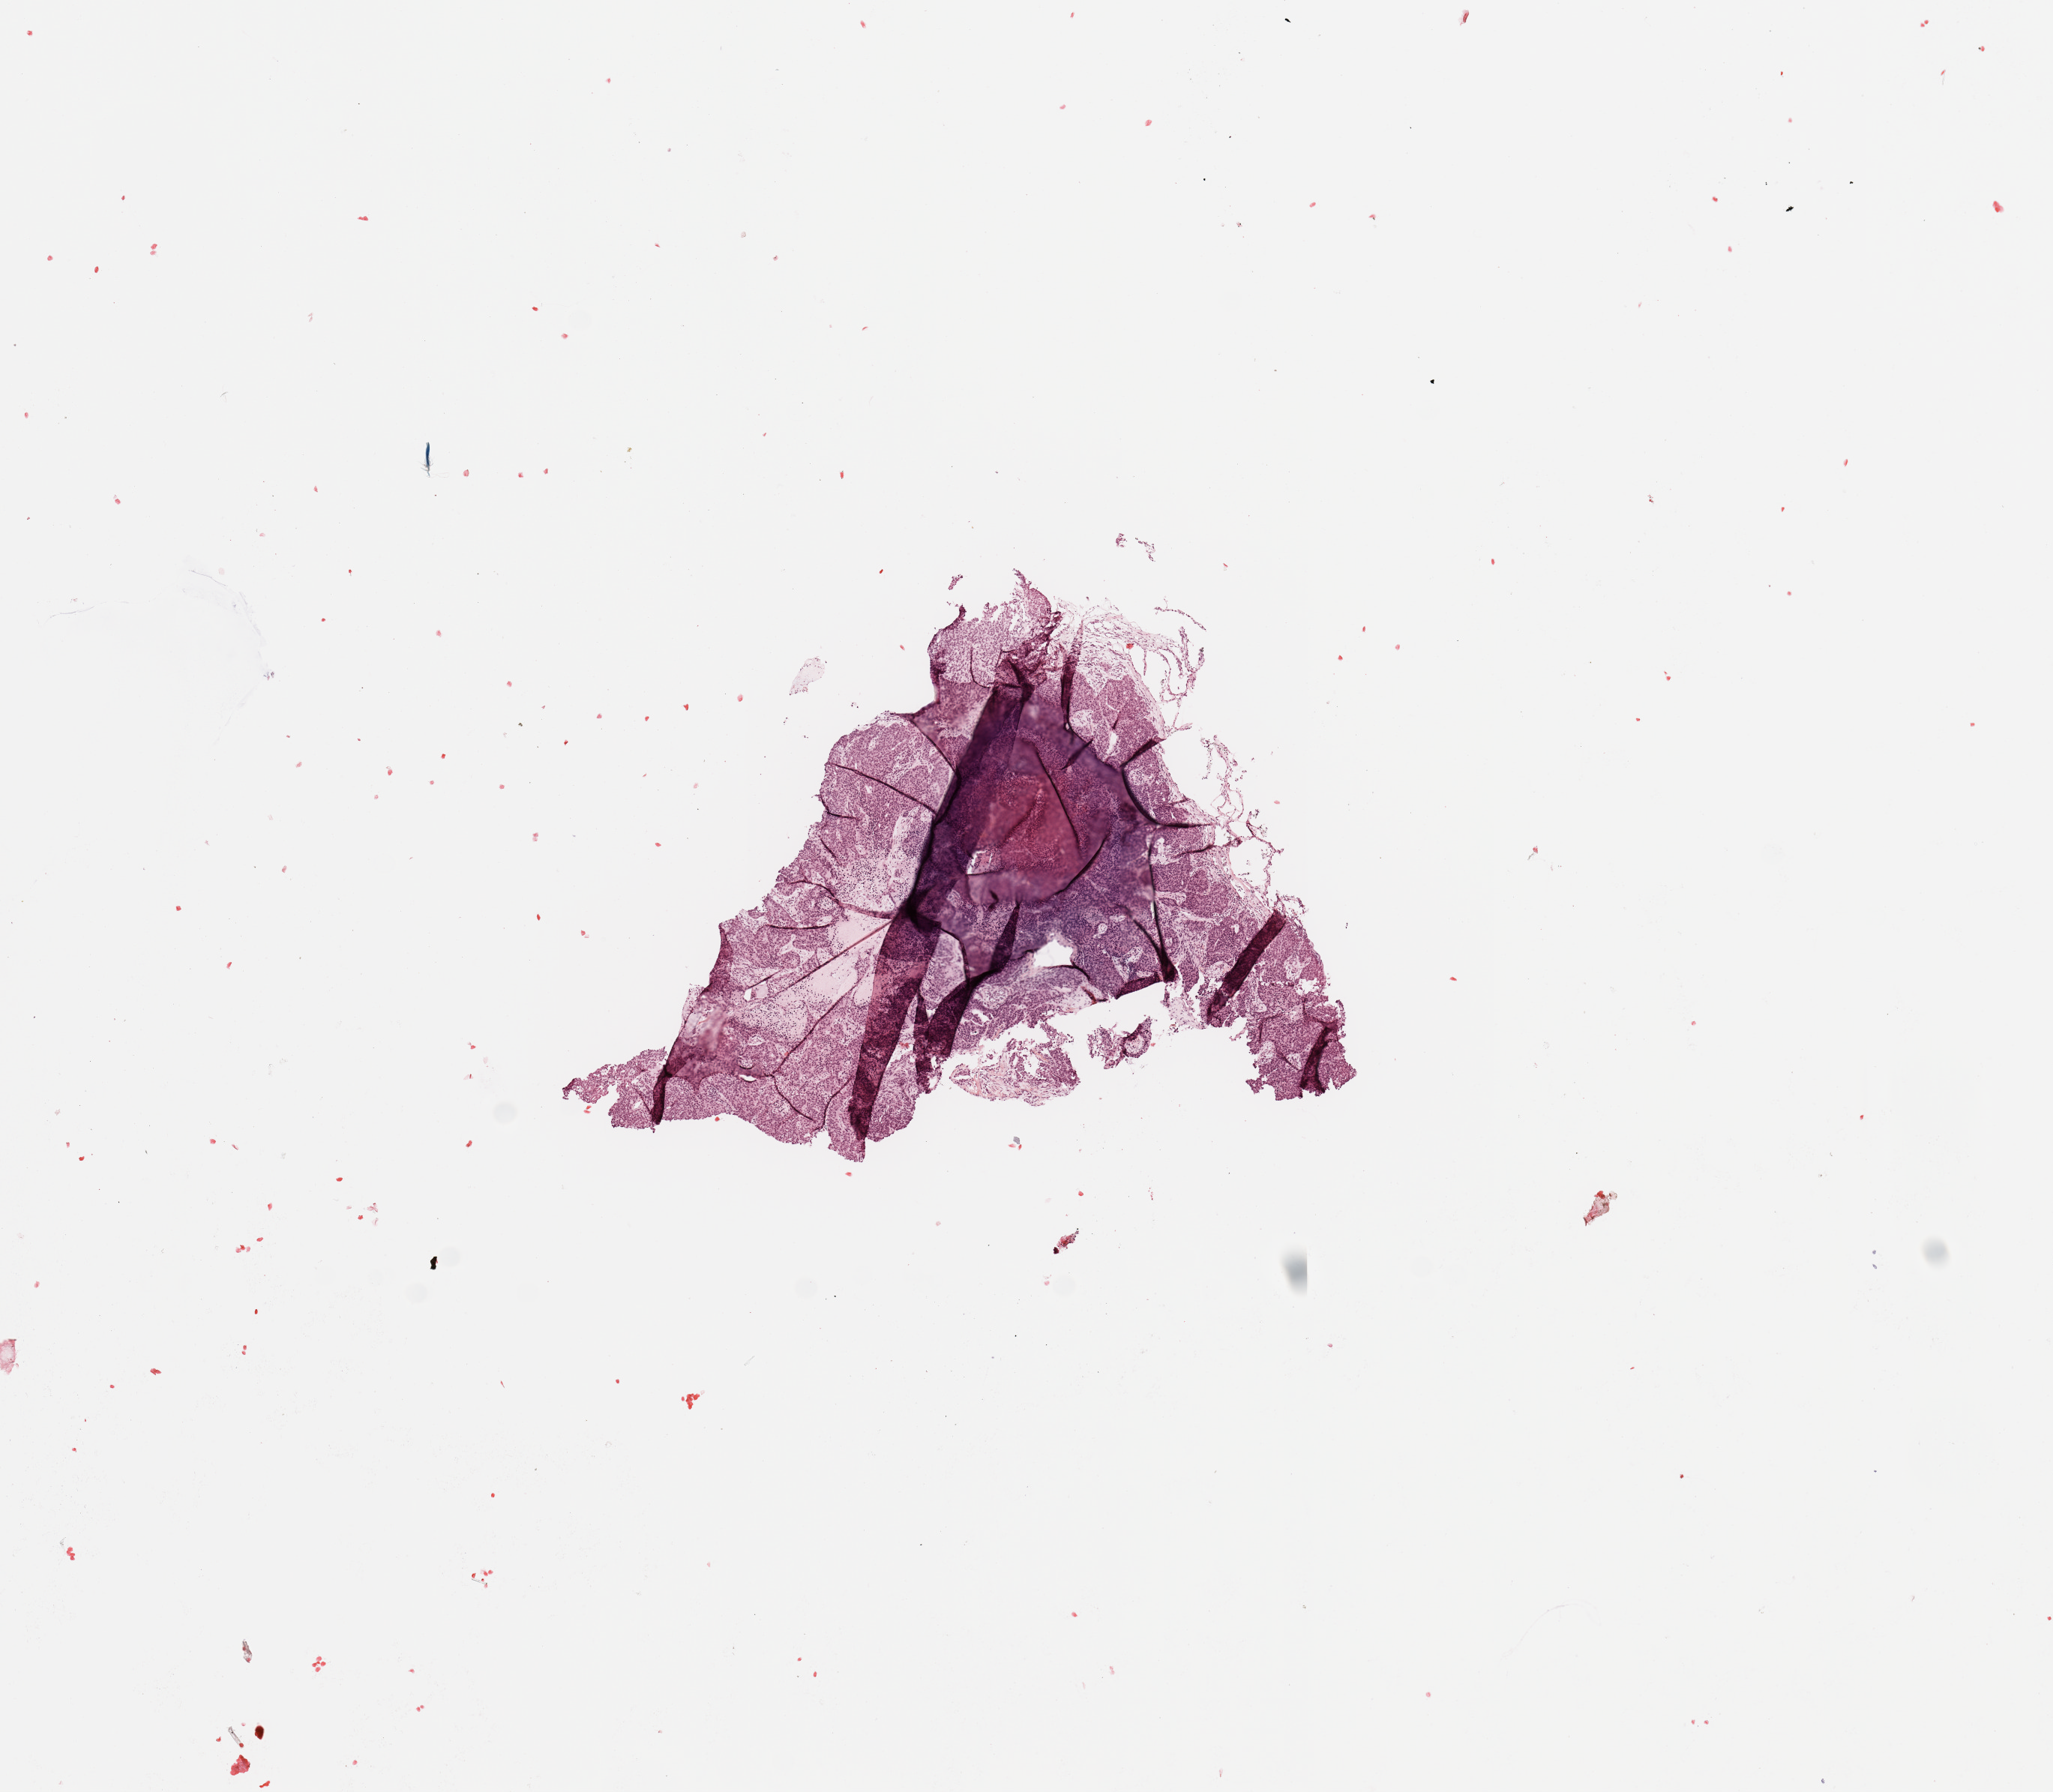
Whole-slide histology image, Hematoxylin and eosin (H&E) stained, low-resolution overview of the scanned area, about 10.8 x 9.5 mm; tumour tissue sample, sampled site: lung. 67-year-old male patient. Histologic grade: GX (grade cannot be assessed). Pathologist review of this section (percent, as recorded): tumour nuclei 80%, necrosis 2%.
Diagnosis: Squamous cell carcinoma, NOS. Primary tumour site (as recorded): right upper lobe. AJCC pathologic stage: IIB.